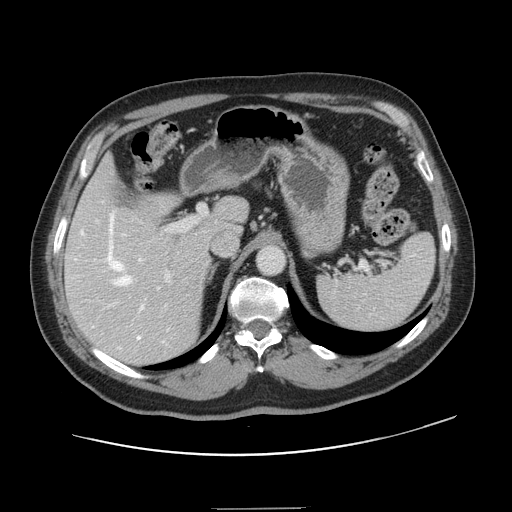
Contrast-enhanced abdominal CT, one axial slice; slice 94 of 143 in the series (ordered by position); 120 kVp; soft-tissue window (W 400 / L 40 HU); 512 × 512 image matrix, field of view 402 × 402 mm. Male patient, age 62 years. From the clinical record (not read from this slice): diagnosis: colorectal cancer liver metastases, imaged before liver resection; multiple liver metastases: yes; largest metastasis: 2.7 cm; chemotherapy before resection: yes.
Outlined on this slice (outlined manually by an expert reader):
- hepatic veins: bounding box (x1, y1, x2, y2) in pixels: (81, 213, 165, 349)
- liver: (66, 161, 247, 364)
- planned liver remnant (the part of the liver to remain after resection): (68, 160, 246, 253)
- portal vein (with intrahepatic branches): (75, 205, 206, 307)